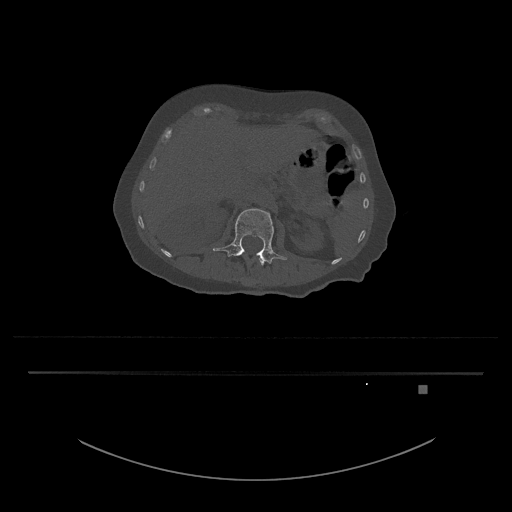
CT including the spine, one axial slice; slice 502 of 797 in the series (ordered by position); reconstruction kernel Br40s/3; 120 kVp; bone window (W 1800 / L 400 HU); 512 × 512 image matrix. Patient: female, 57 years. Case-level facts recorded for this patient, not image findings: primary cancer: cervical.
Outlined on this slice (semi-automatic segmentation, software-assisted and operator-edited):
- L1 vertebra: bounding box <244,251,265,265> (left, top, right, bottom; pixels)